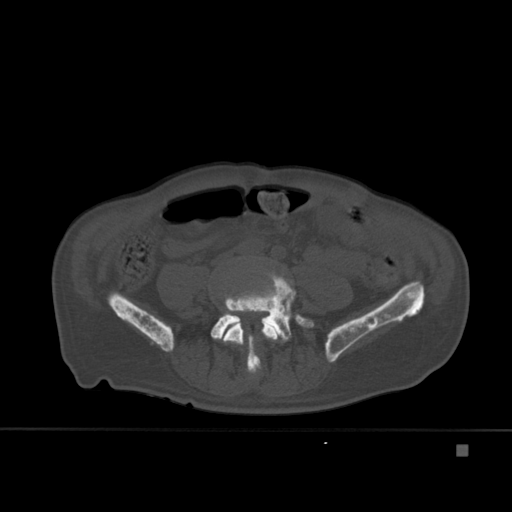
CT including the spine, one axial slice. Slice 111 of 451 in the series (ordered by position). Bone window (W 1800 / L 400 HU). 1.5 mm slice thickness. 512 × 512 image matrix. Patient: male, 75 years. Case-level facts recorded for this patient, not image findings: primary cancer: prostate.
Structures marked on this image (semi-automatic segmentation, software-assisted and operator-edited):
- L4 vertebra: bounding box (x1, y1, x2, y2) in pixels: (223, 311, 278, 374)
- L5 vertebra: (210, 270, 314, 370)
- T7 vertebra: (266, 309, 279, 324)